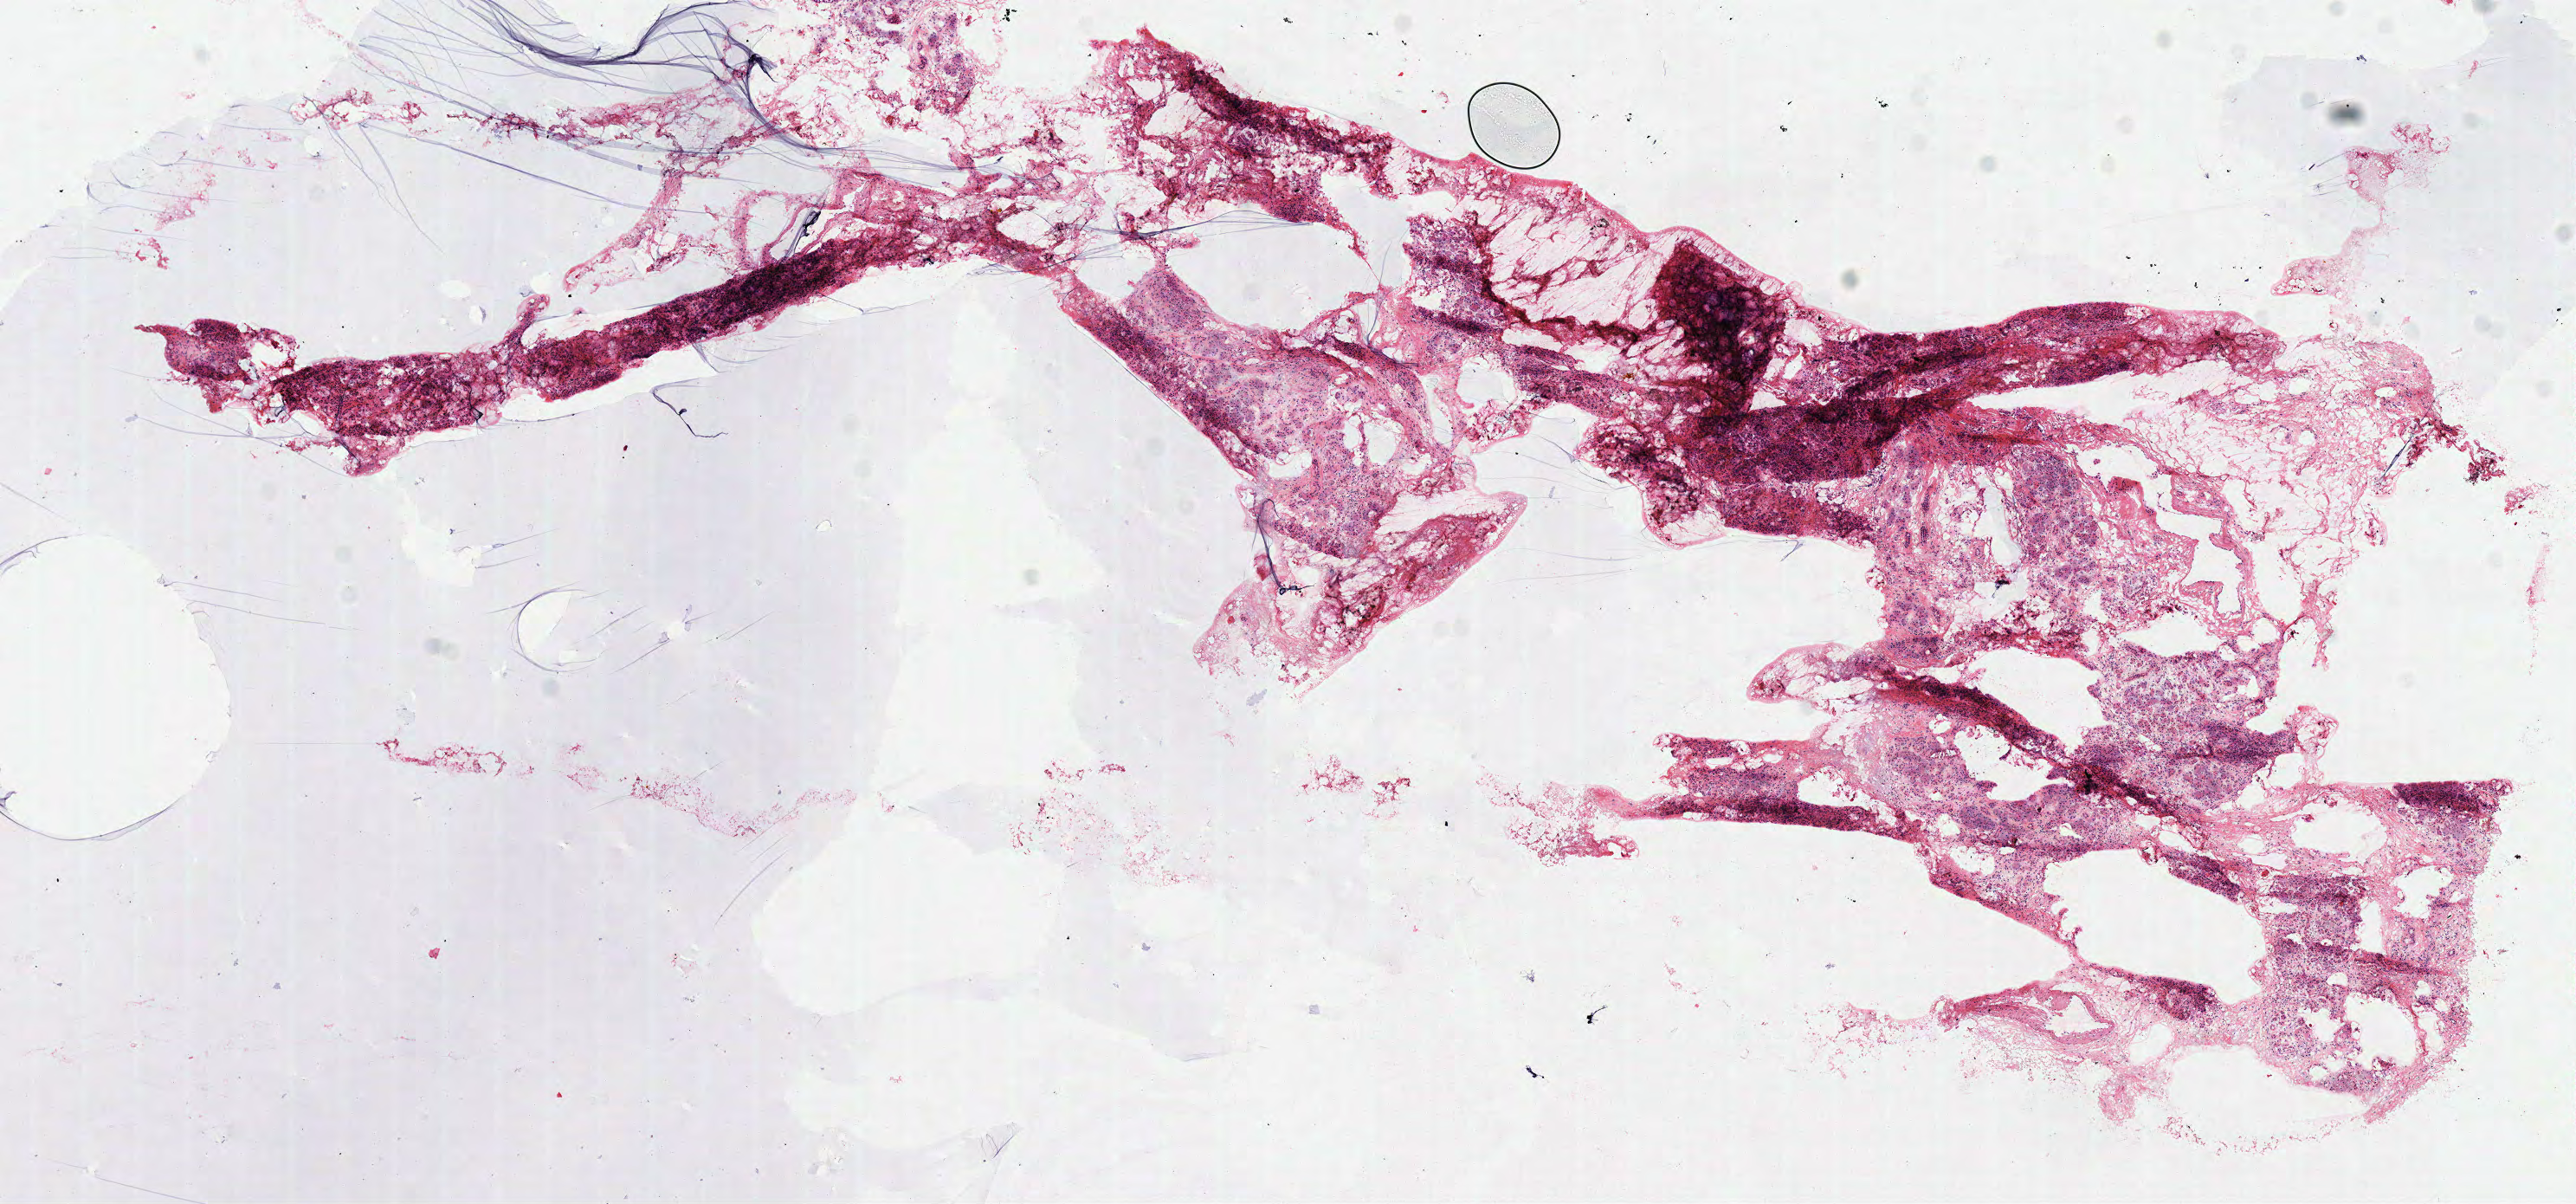
Digitized H&E tissue section (whole slide), shown as a low-resolution overview of the whole scanned area (about 11.7 x 5.5 mm, acquisition: 40x scan); frozen section from the top of the tissue portion; sample: solid tissue normal (non-tumour tissue), pancreas. Male, age 81 years at initial diagnosis.
This section: solid tissue normal (non-tumour) sample from the same patient. Patient diagnosis: Infiltrating duct carcinoma, NOS (head of pancreas).